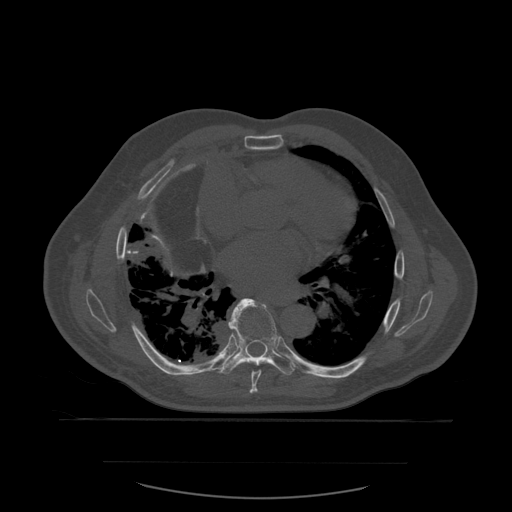
CT including the spine, one axial slice; slice 369 of 590 in the series (ordered by position); bone window (W 1800 / L 400 HU); 1.25 mm slice thickness; 512 × 512 image matrix. Patient age 71 years. Case-level facts recorded for this patient, not image findings: primary cancer: lung.
Annotated regions visible in this slice (semi-automatically segmented with operator editing):
- T7 vertebra: box from (x=250, y=370) to (x=262, y=394) px
- T8 vertebra: (x=221, y=299)–(x=295, y=376)